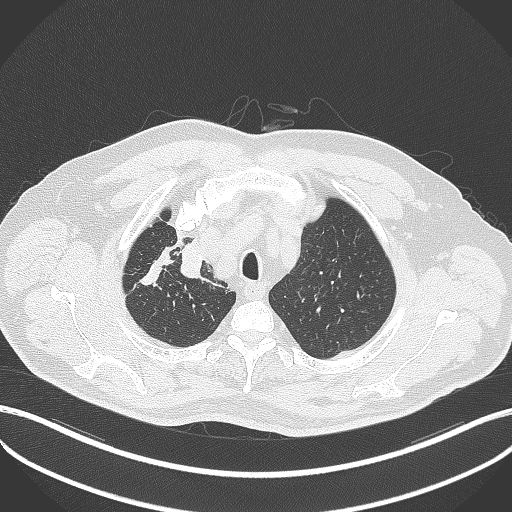
Chest CT, one axial slice; reconstruction kernel B70f; lung window (W 1500 / L -600 HU); 1 mm slice thickness; 512 × 512 image matrix, field of view 400 × 400 mm. Male patient, age 60 years. From the clinical record (not read from this slice): clinical TNM (as recorded): T1b N1 M0.
Structures marked on this image (rectangle marked by the reading radiologist):
- lung tumour (recorded histology: squamous cell carcinoma): bounding box (x1, y1, x2, y2) in pixels: (176, 236, 212, 278)